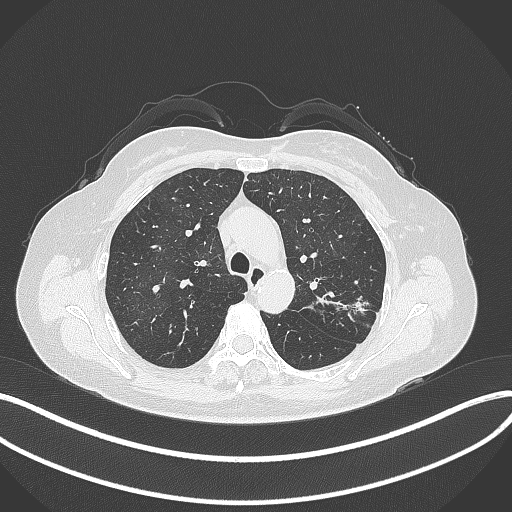
Chest CT, one axial slice; slice 235 of 319 in the series (ordered by position); 120 kVp; lung window (W 1500 / L -600 HU); 512 × 512 image matrix, field of view 400 × 400 mm. Female patient, age 60 years. From the clinical record (not read from this slice): clinical TNM (as recorded): T1c N0 M0.
Structures marked on this image (bounding box drawn by a radiologist):
- lung tumour (recorded histology: adenocarcinoma): bounding box [x1, y1, x2, y2] px = [344, 291, 369, 319]